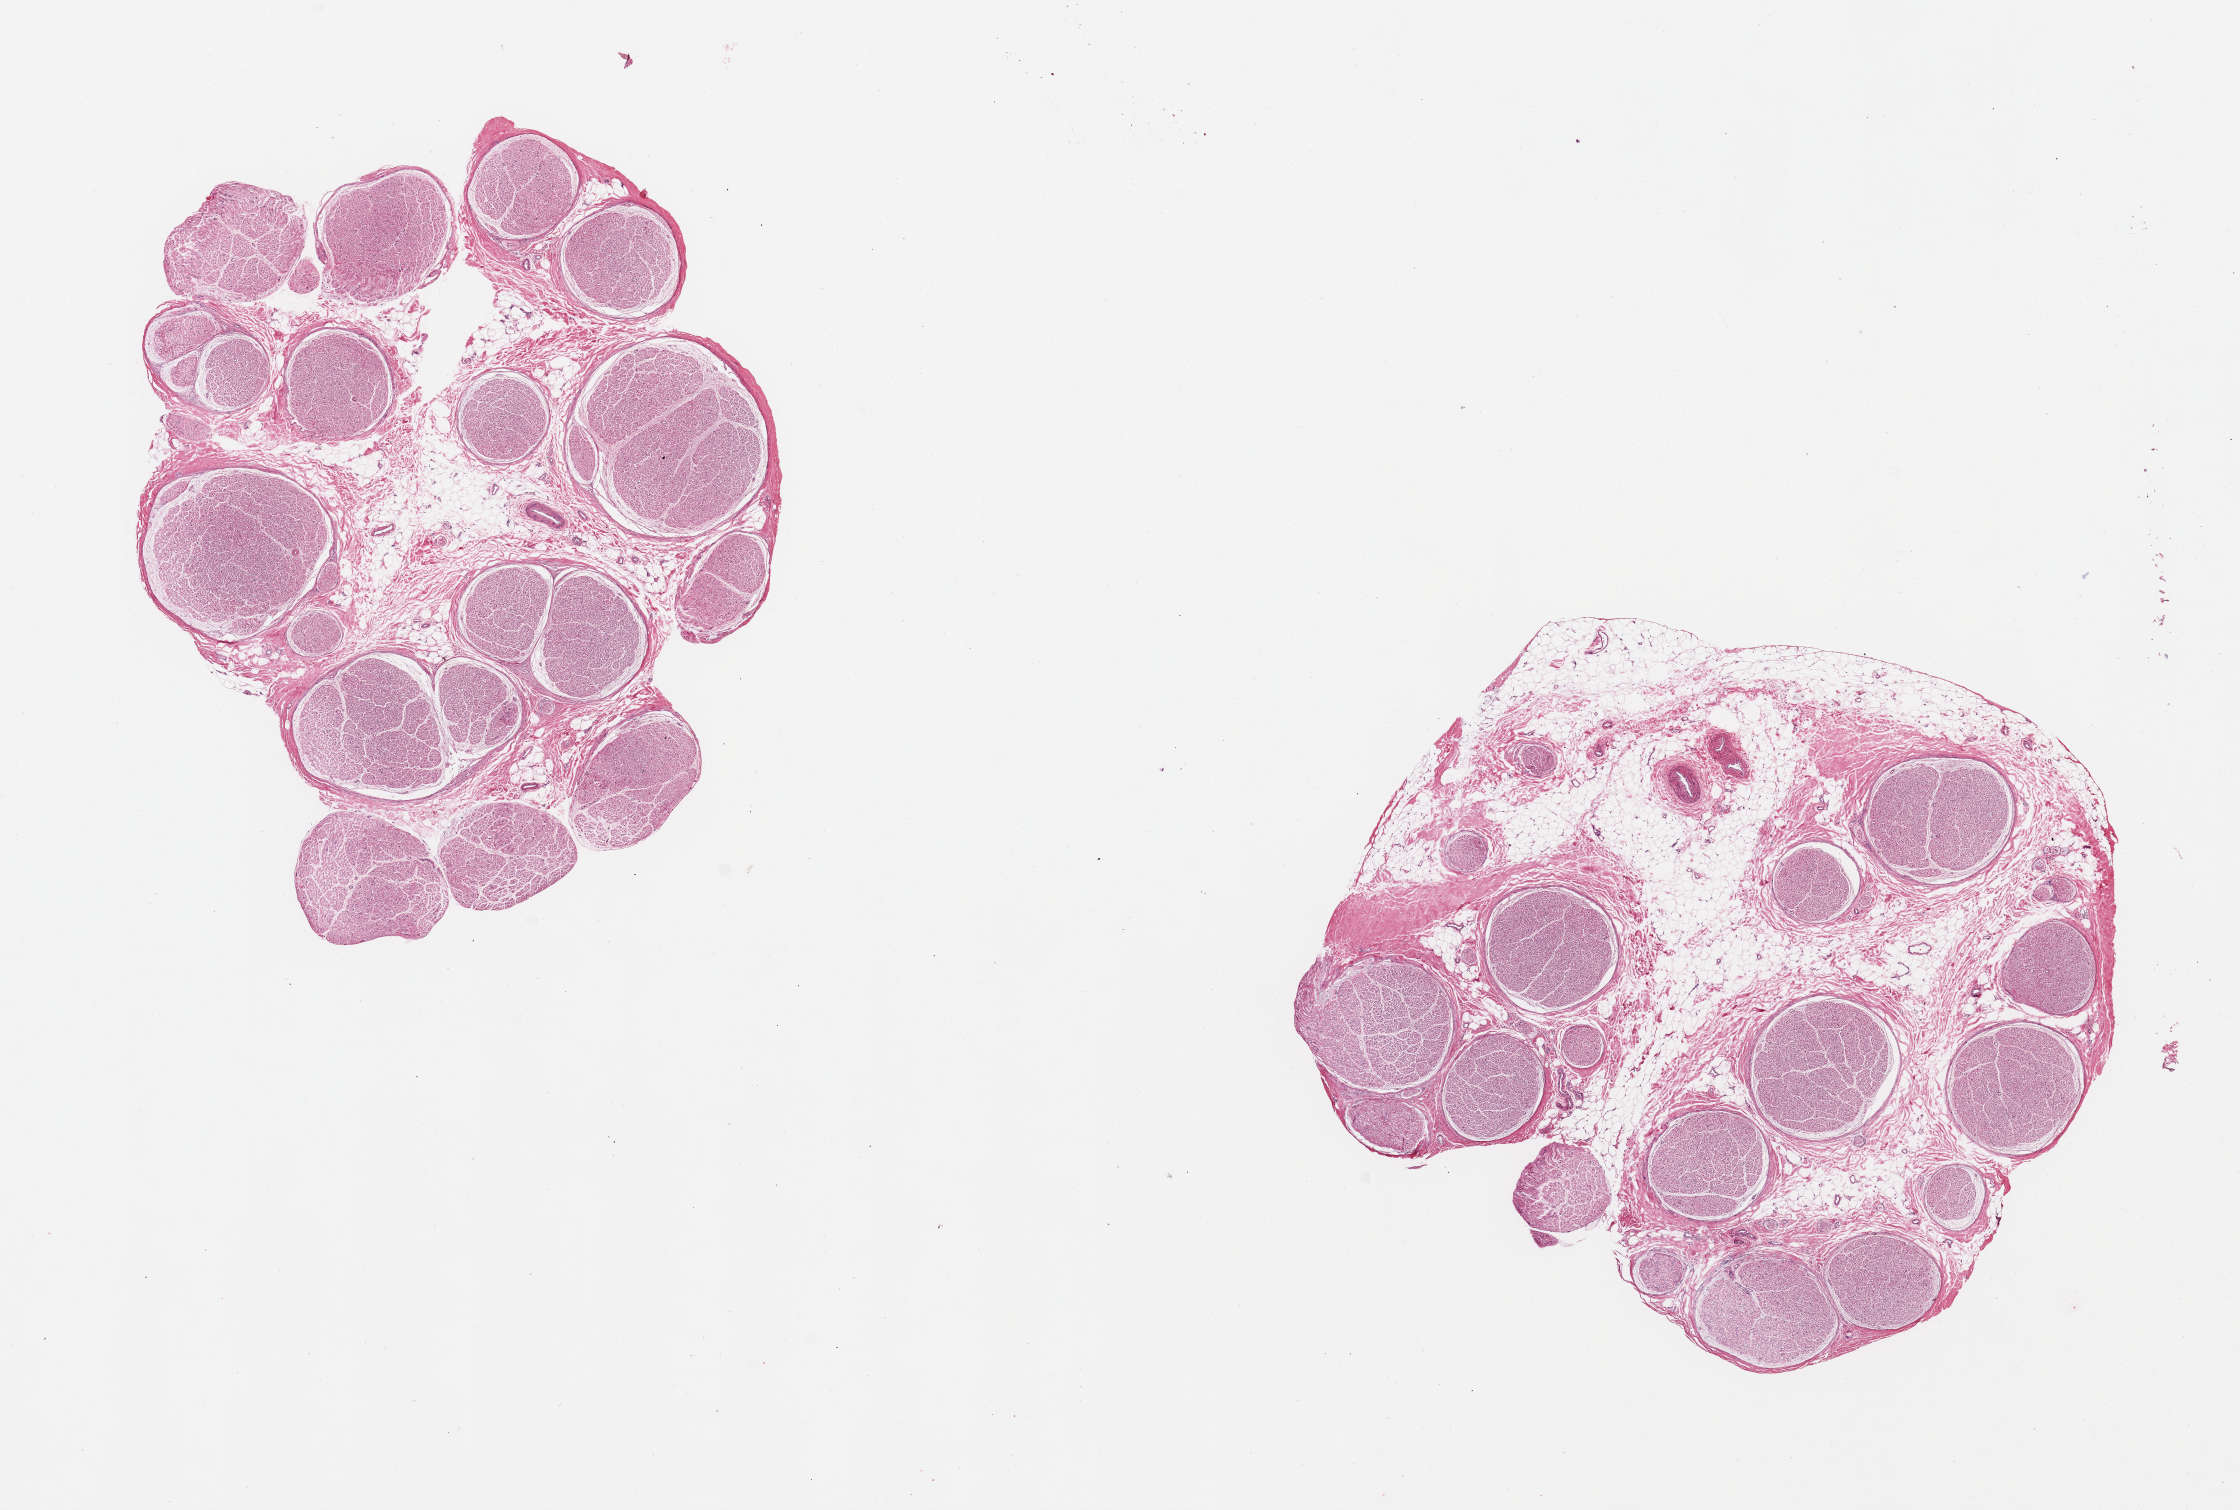
Digitized haematoxylin and eosin-stained section — a low-resolution overview of the entire scanned area, about 17.7 x 11.9 mm (acquisition: 20x scan). PAXgene-fixed, paraffin-embedded tissue. Sampled site (target tissue): tibial nerve. Tissue donor sample. Donor sex: male.
Pathologist's review note for this sample: 2 pieces; includes 20 and 40% internal/external fat.